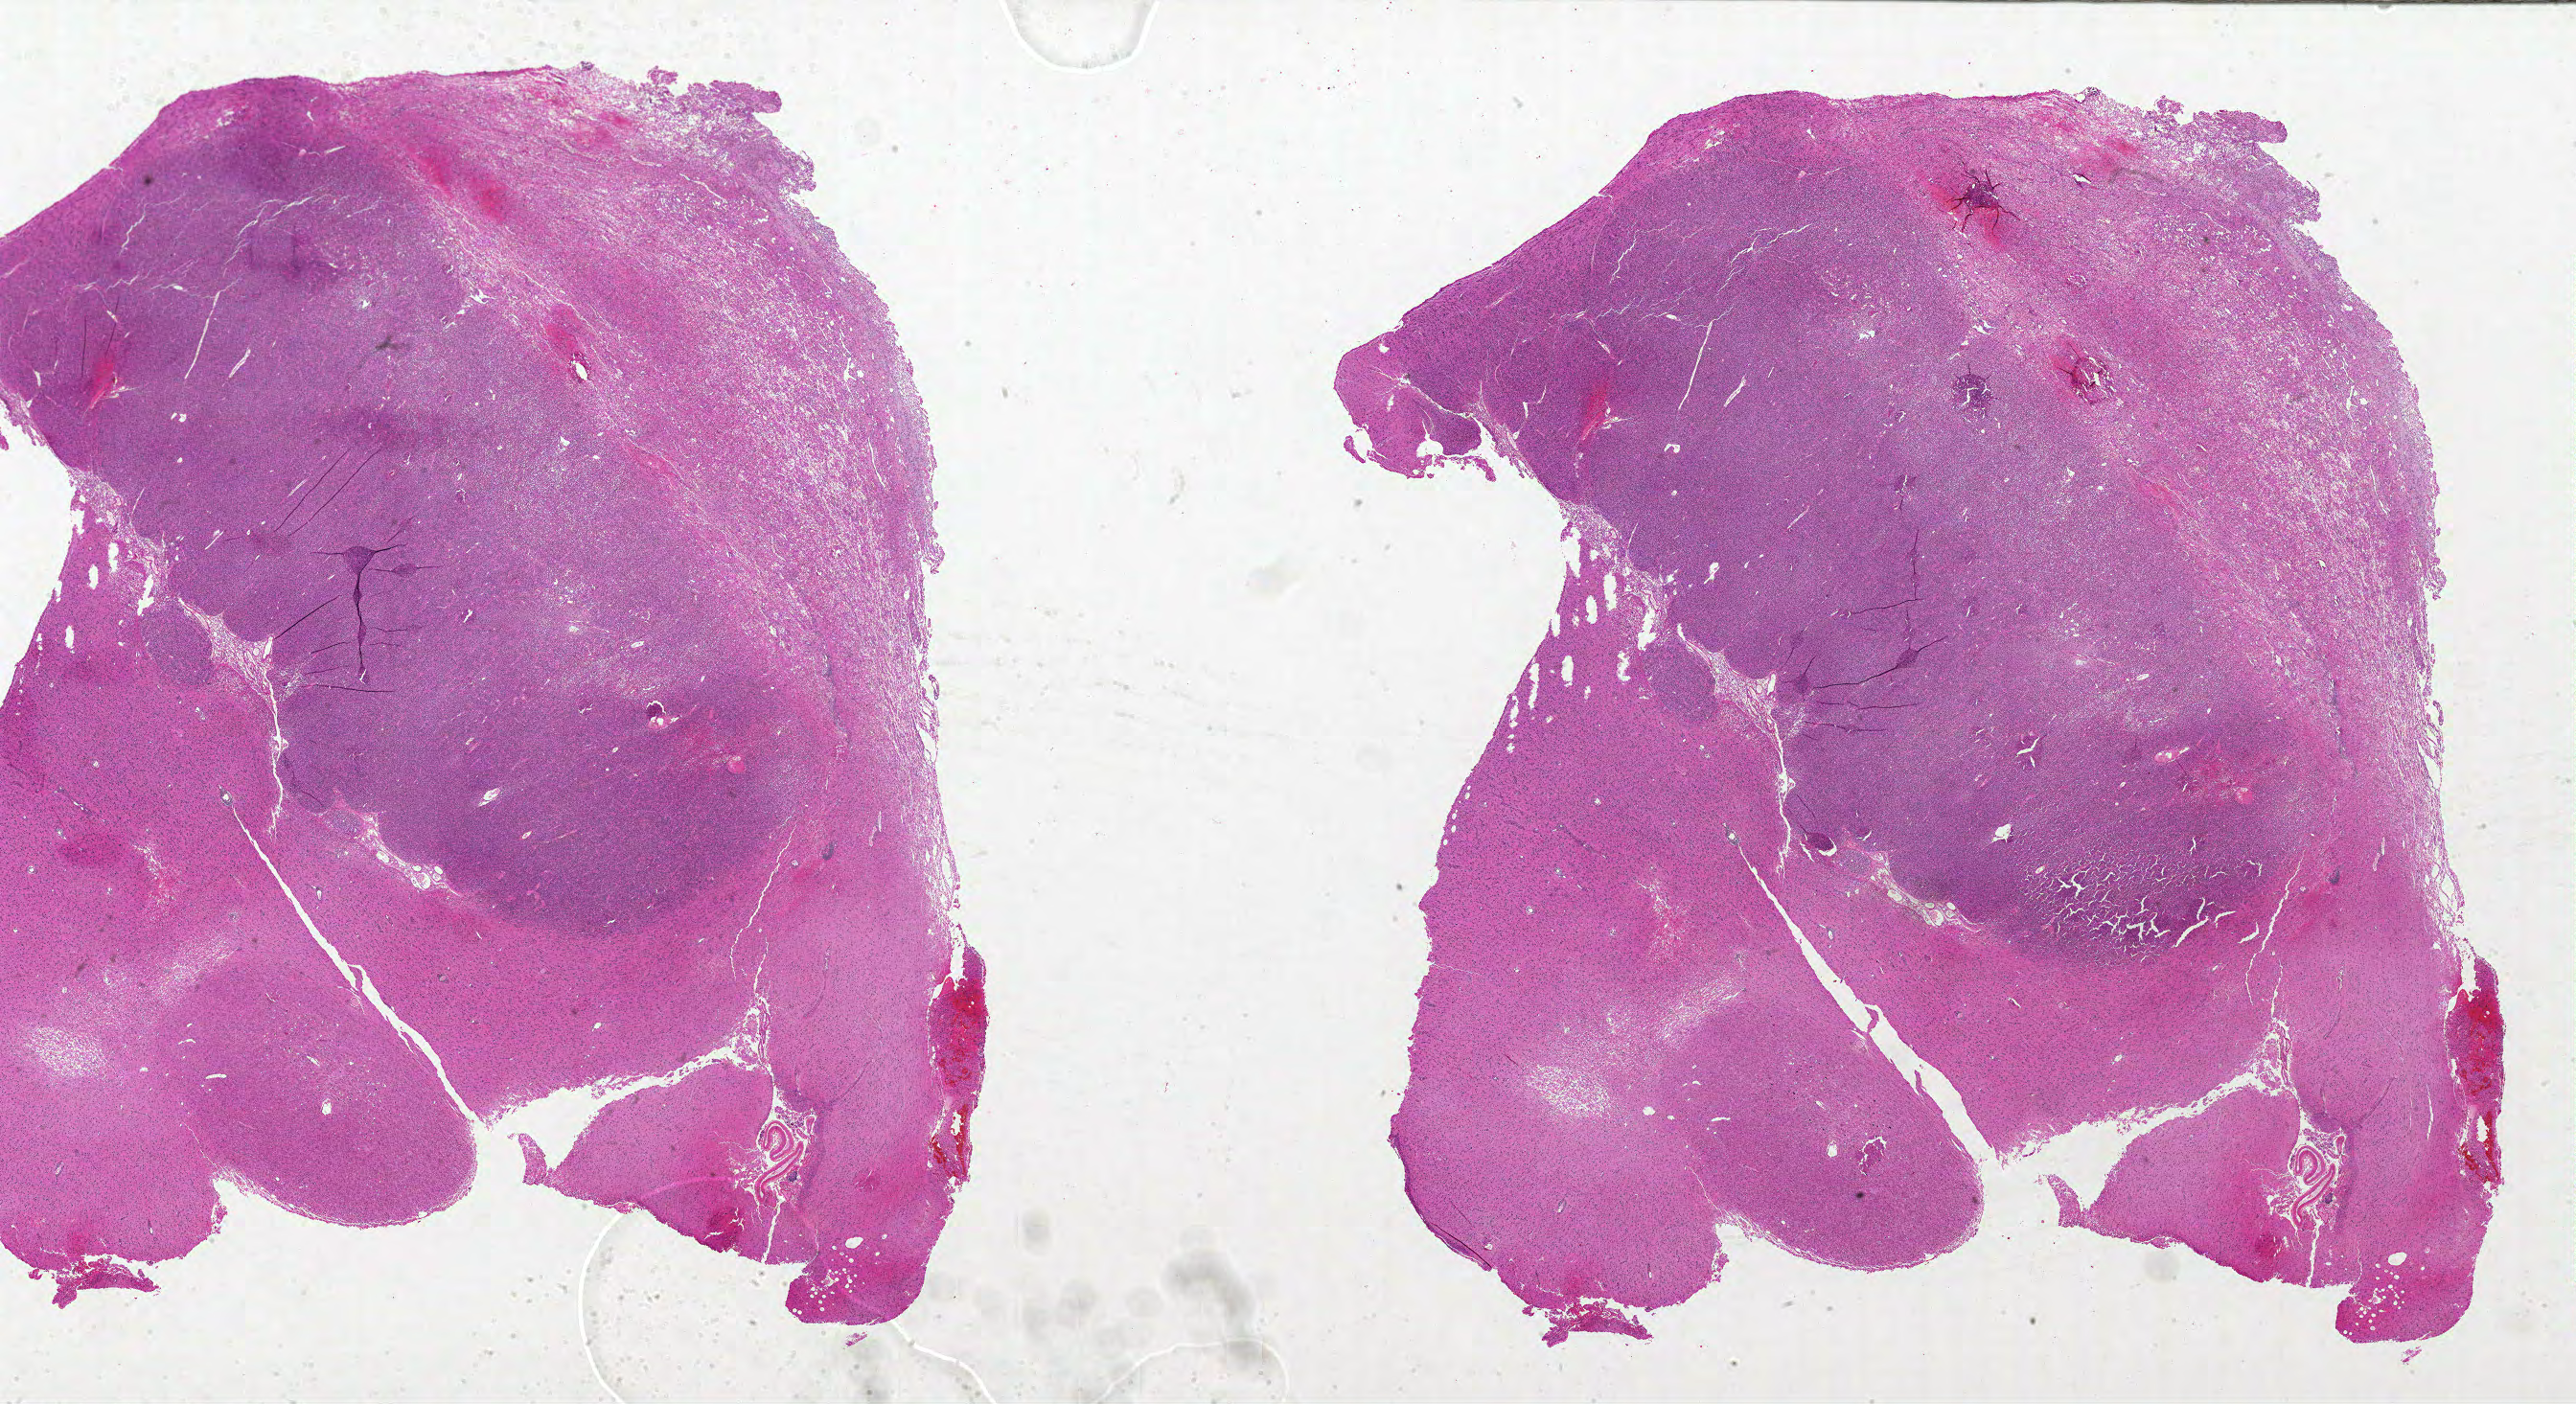
Digitized H&E-stained tissue section (whole slide), low-resolution overview of the scanned area, about 43.0 x 23.4 mm (acquisition: 20x scan), formalin-fixed paraffin-embedded (FFPE) diagnostic section, primary tumour sample from the brain. Female patient; age at initial diagnosis 34 years.
• diagnosis: Glioblastoma